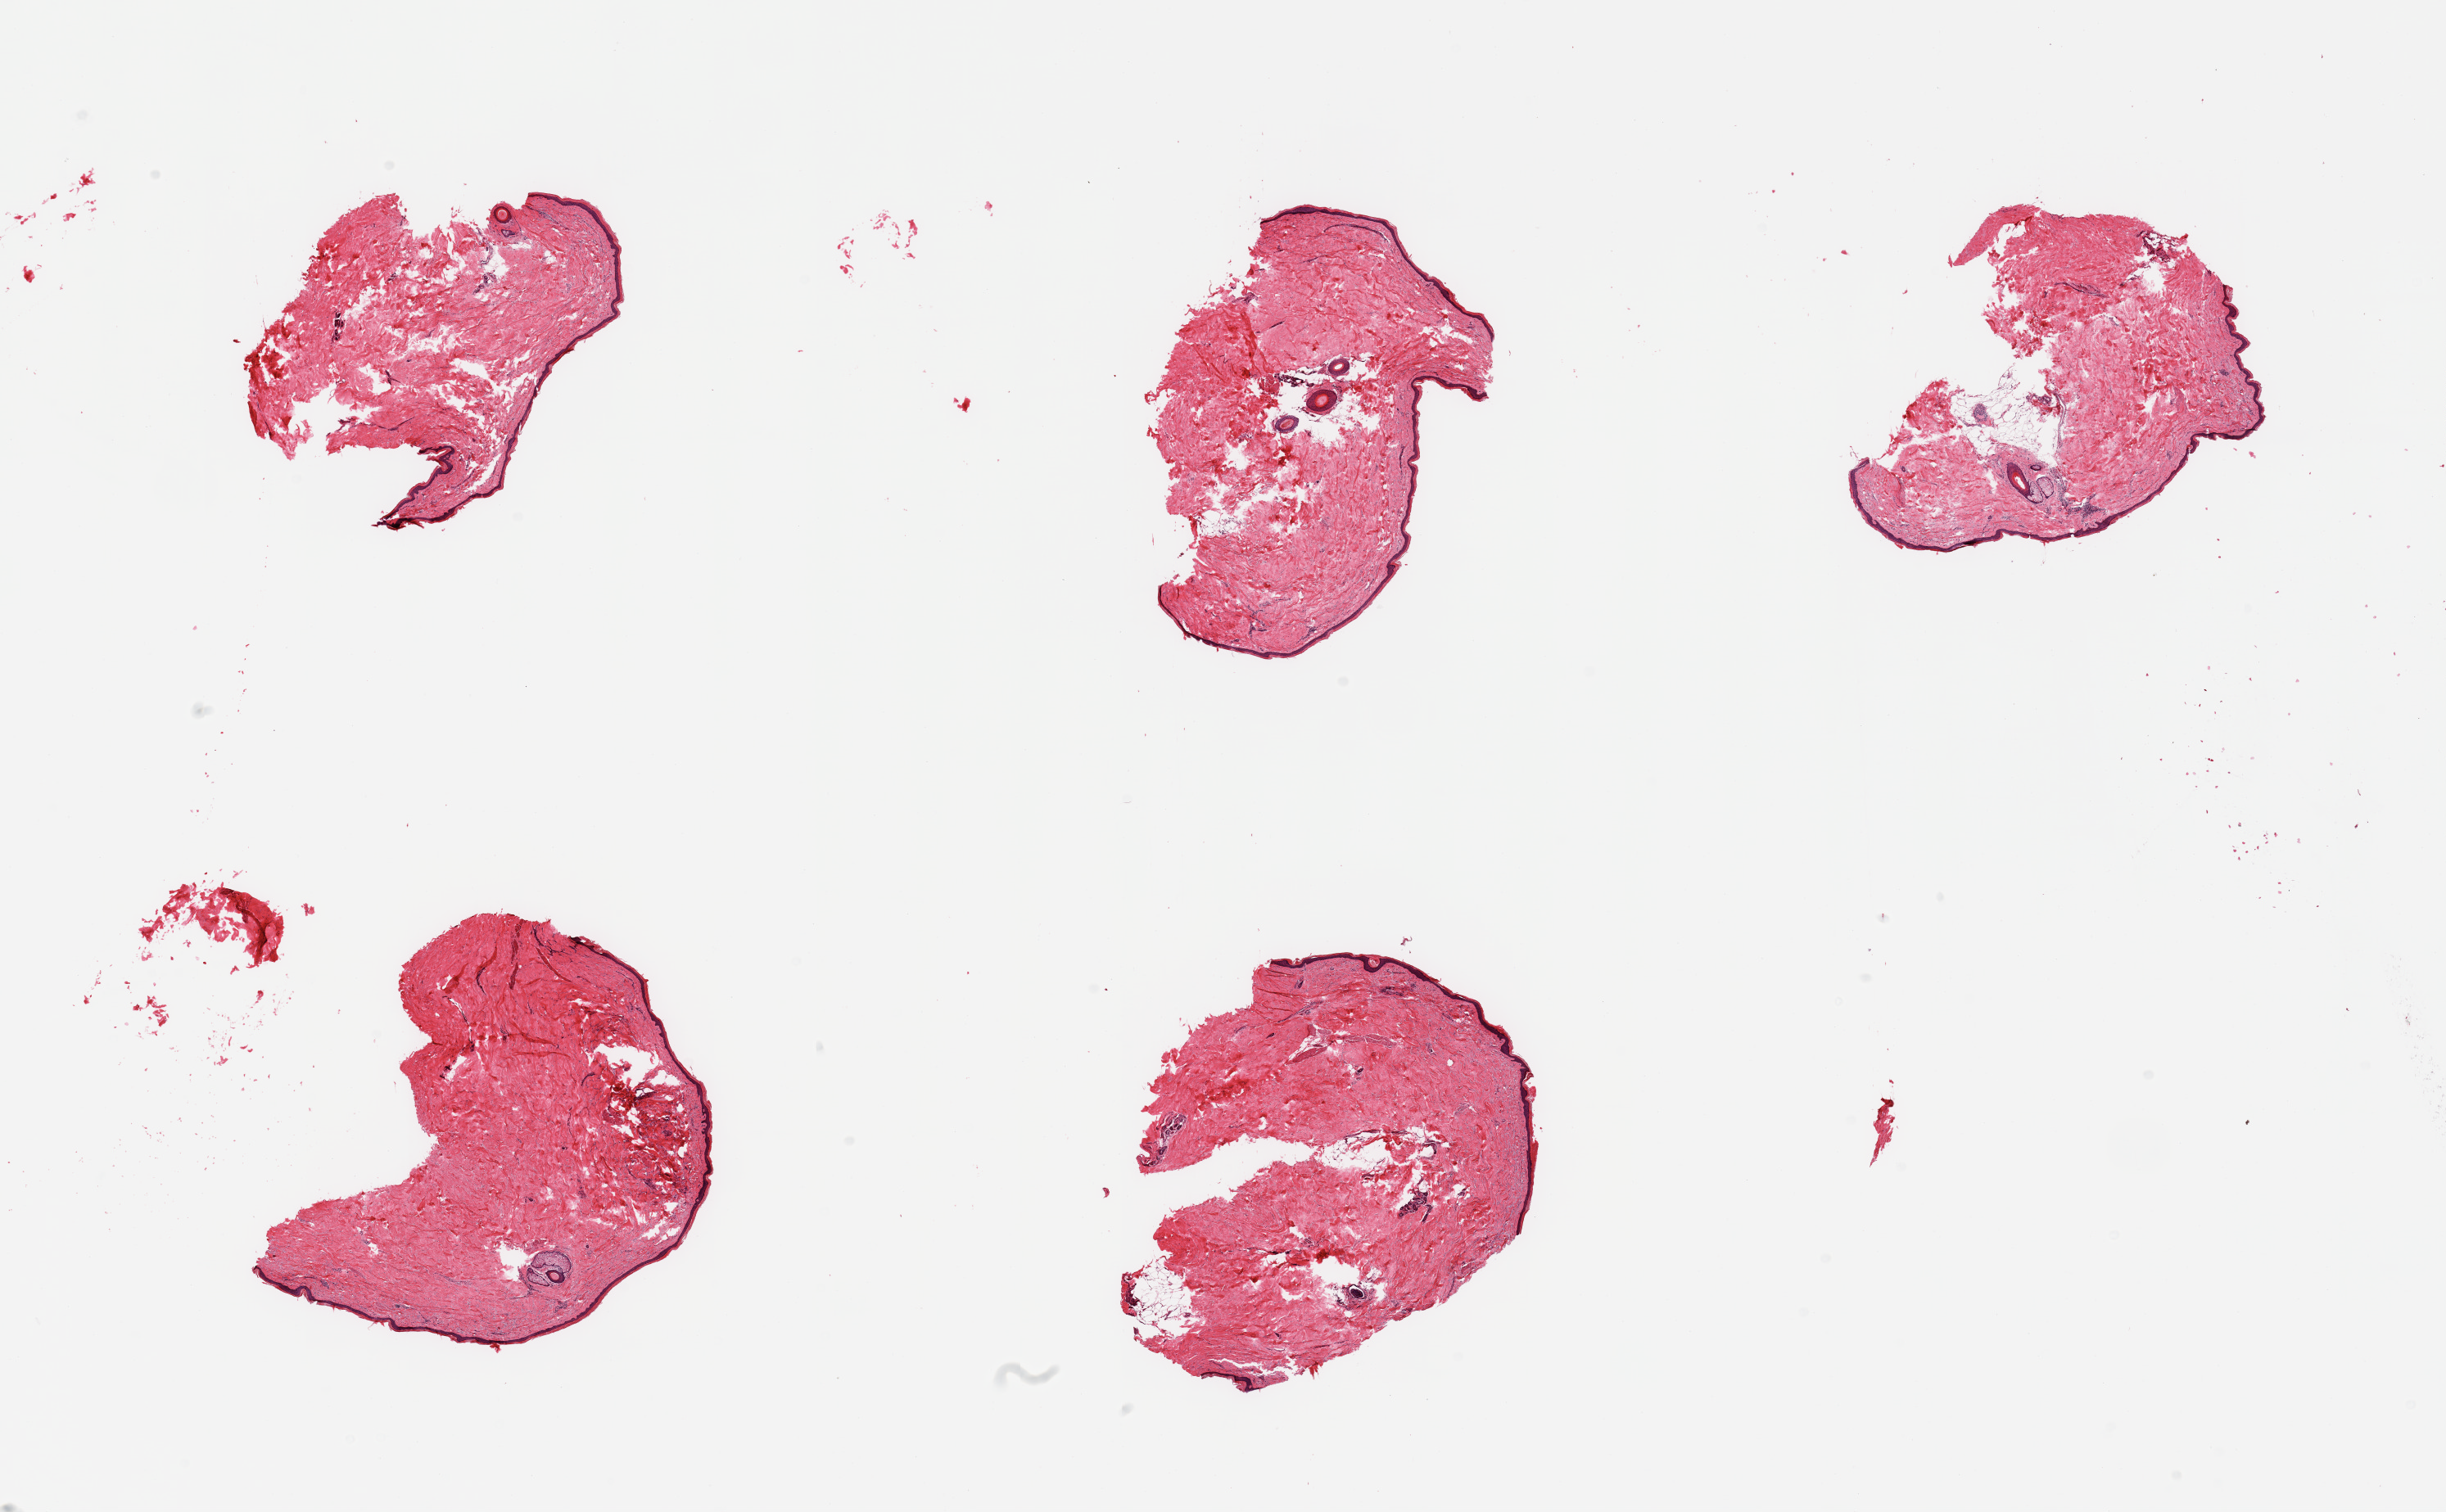
Haematoxylin and eosin whole-slide image, low-resolution overview of the scanned area, about 23.6 x 14.6 mm; PAXgene-fixed, paraffin-embedded tissue; target tissue: skin of lower leg; donor tissue sample. Donor sex: male.
Pathologist's review note for this sample: 5 pieces; ~10% to 20% internal fat; epidermis is ~30 microns thick.